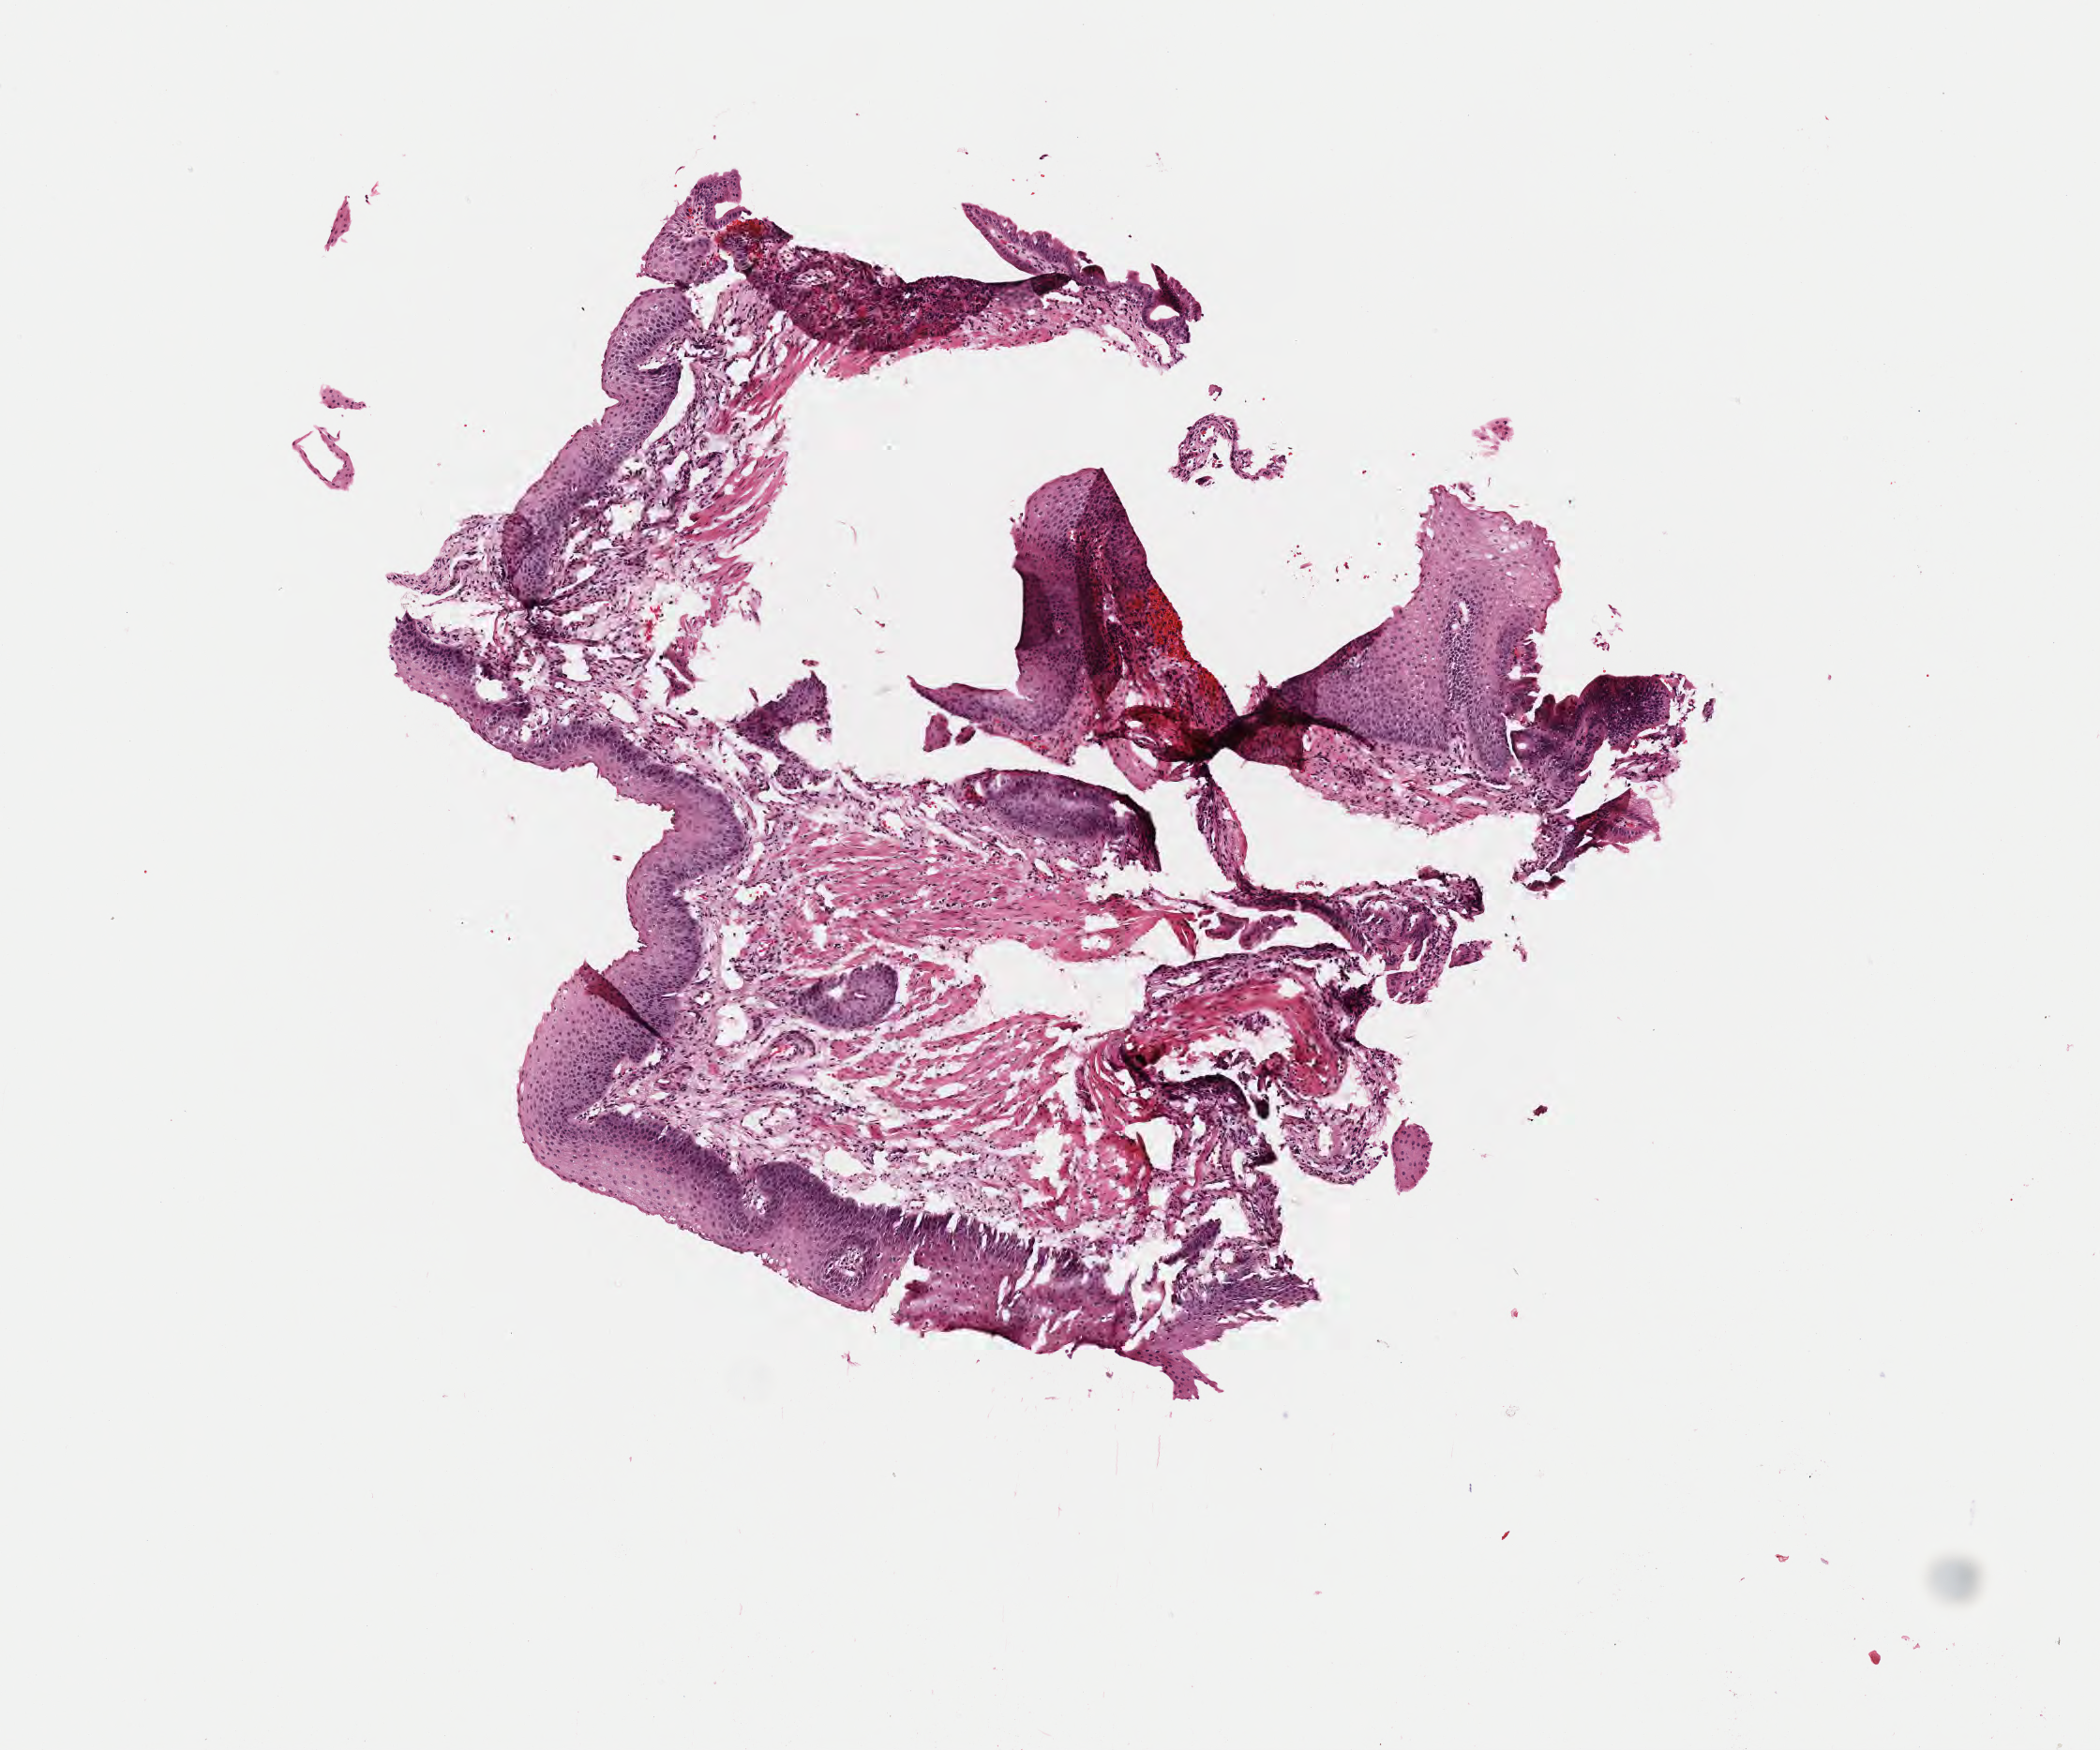
Whole-slide image, hematoxylin and eosin (H&E) stain — shown as a low-resolution overview of the whole scanned area (about 4.5 x 3.8 mm). Formalin-fixed, paraffin-embedded (FFPE) tissue. Specimen: normal-tissue sample (non-tumor) from a patient with burkitt lymphoma, NOS. Patient: female, age at initial diagnosis 6 years. Pathologist review of this section (percent, as recorded): tumor cells 0%, tumor nuclei 0%, stromal cells 70%, necrosis 0%, normal cells 30%. Inflammatory infiltration, as recorded: lymphocyte infiltration 30%, monocyte infiltration 10%, neutrophil infiltration 10%.
This section: non-tumor tissue sample; the patient's diagnosis is given above. Section: top of the tissue portion.